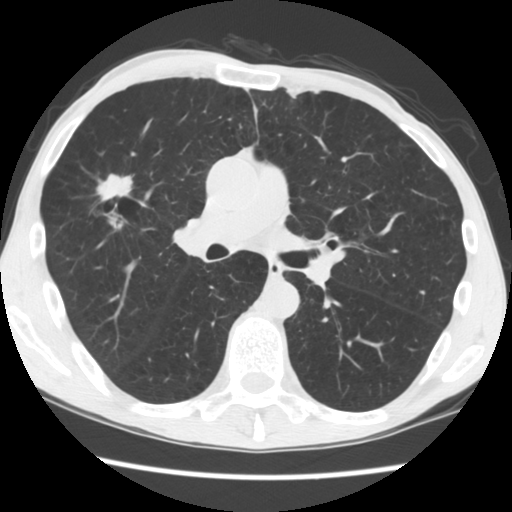
Low-dose screening chest CT, one axial slice. Slice 100 of 181 in the series (ordered by position). 120 kVp. Lung window (W 1500 / L -600 HU). 512 × 512 image matrix.
Outlined on this slice (manually delineated by an expert):
- lesion 1 (tumor, upper lobe of right lung): bounding box <96,174,133,229> (left, top, right, bottom; pixels)